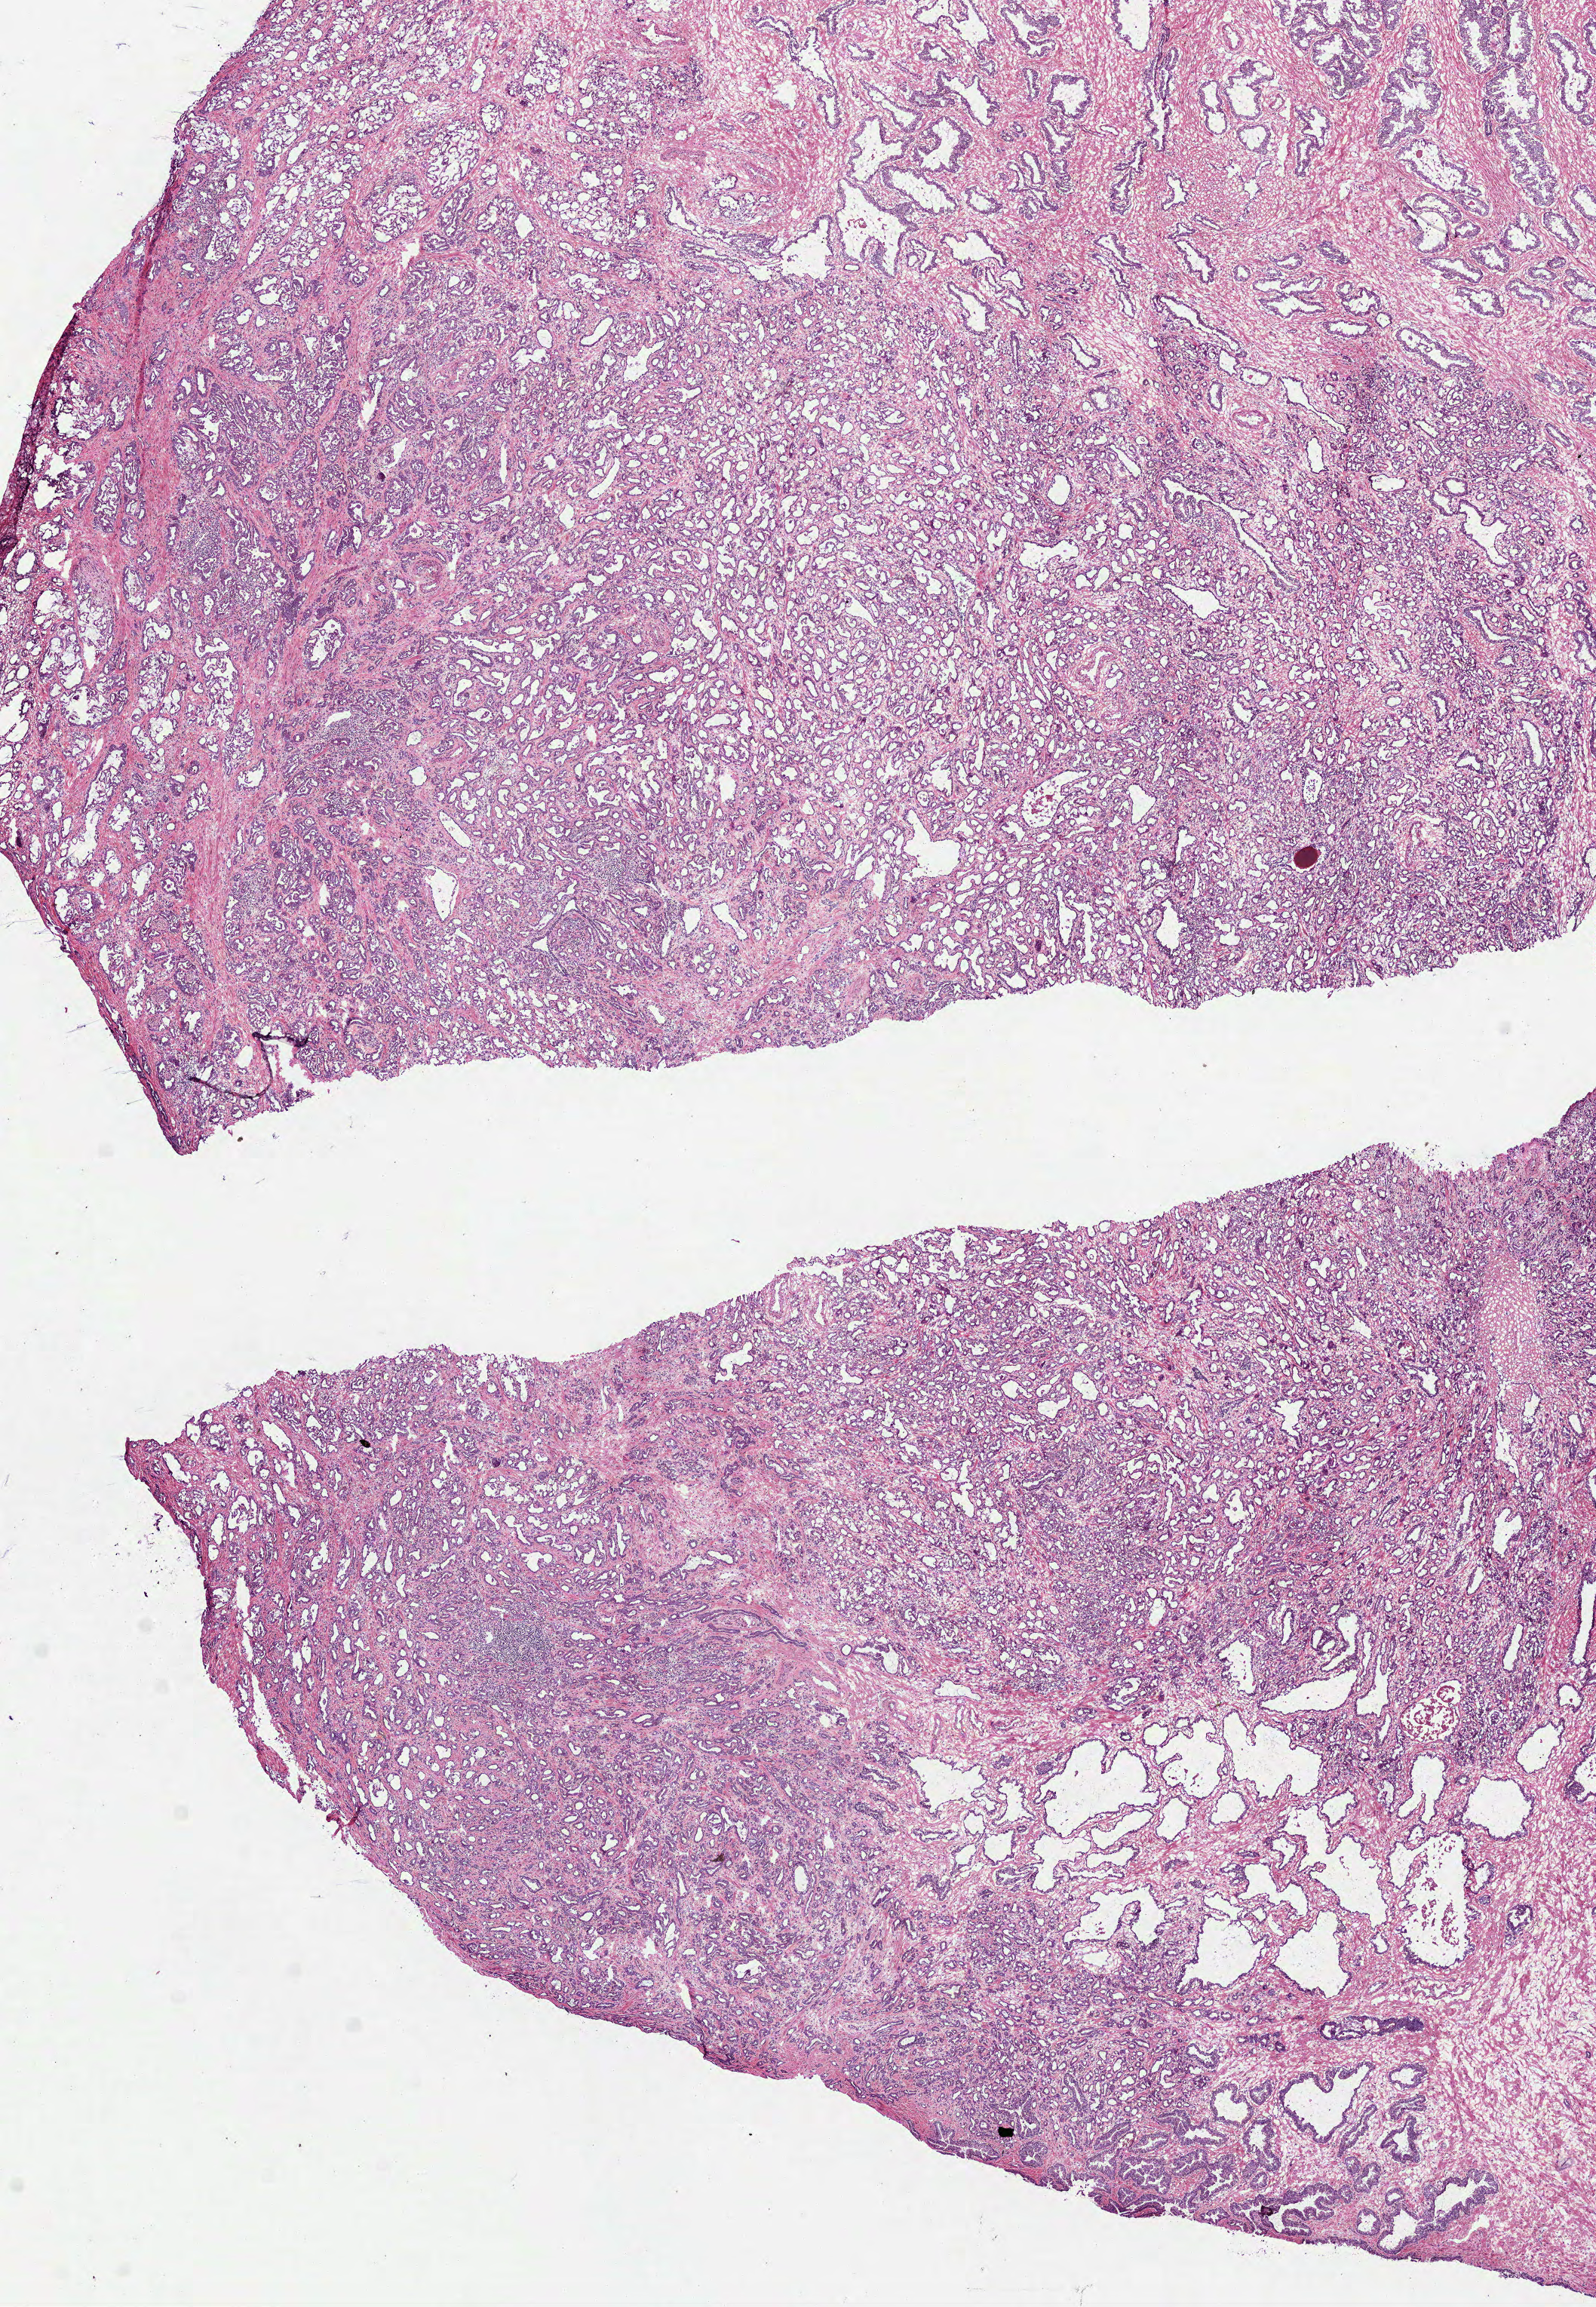
H&E whole-slide image — low-resolution overview of the scanned area, about 8.5 x 12.3 mm; frozen section from the bottom of the tissue portion; sample: primary tumour, prostate. Patient: male, age at initial diagnosis 53 years. Gleason score: 7 (3+4). Slide review estimates, as recorded: tumour cells 75%, tumour nuclei 80%, normal cells 15%, stromal cells 10%, necrosis 0%. Infiltration values recorded for this section: lymphocyte infiltration 1%, monocyte infiltration 0%, neutrophil infiltration 0%.
Lymph nodes positive (case pathology): 0 of 14 examined. Laterality: bilateral. Diagnosis: Acinar cell carcinoma (prostate gland).